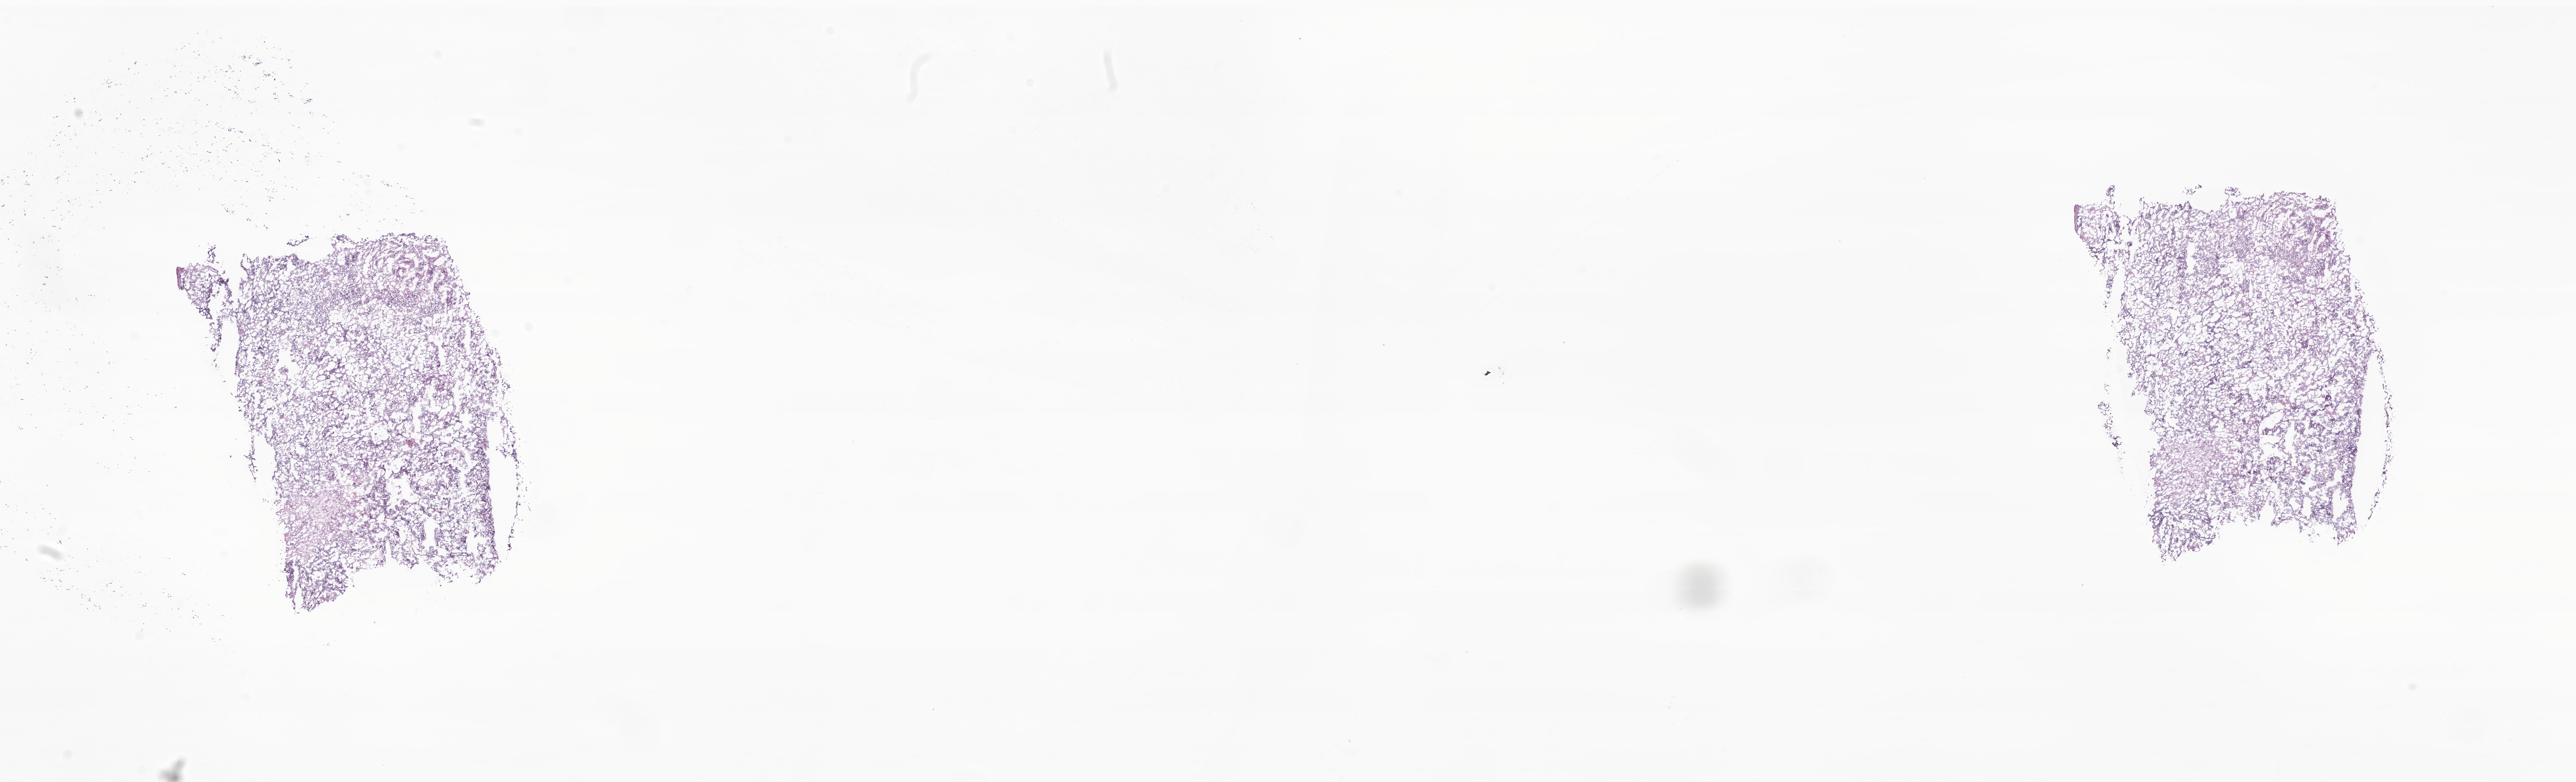
Digitized hematoxylin and eosin (H&E)-stained section of tumor tissue from the kidney — whole scanned area (about 27.8 x 8.4 mm) shown as a low-resolution overview; frozen section (OCT-embedded). Patient male; age 61 months.
Diagnosis: Neuroblastoma, NOS.